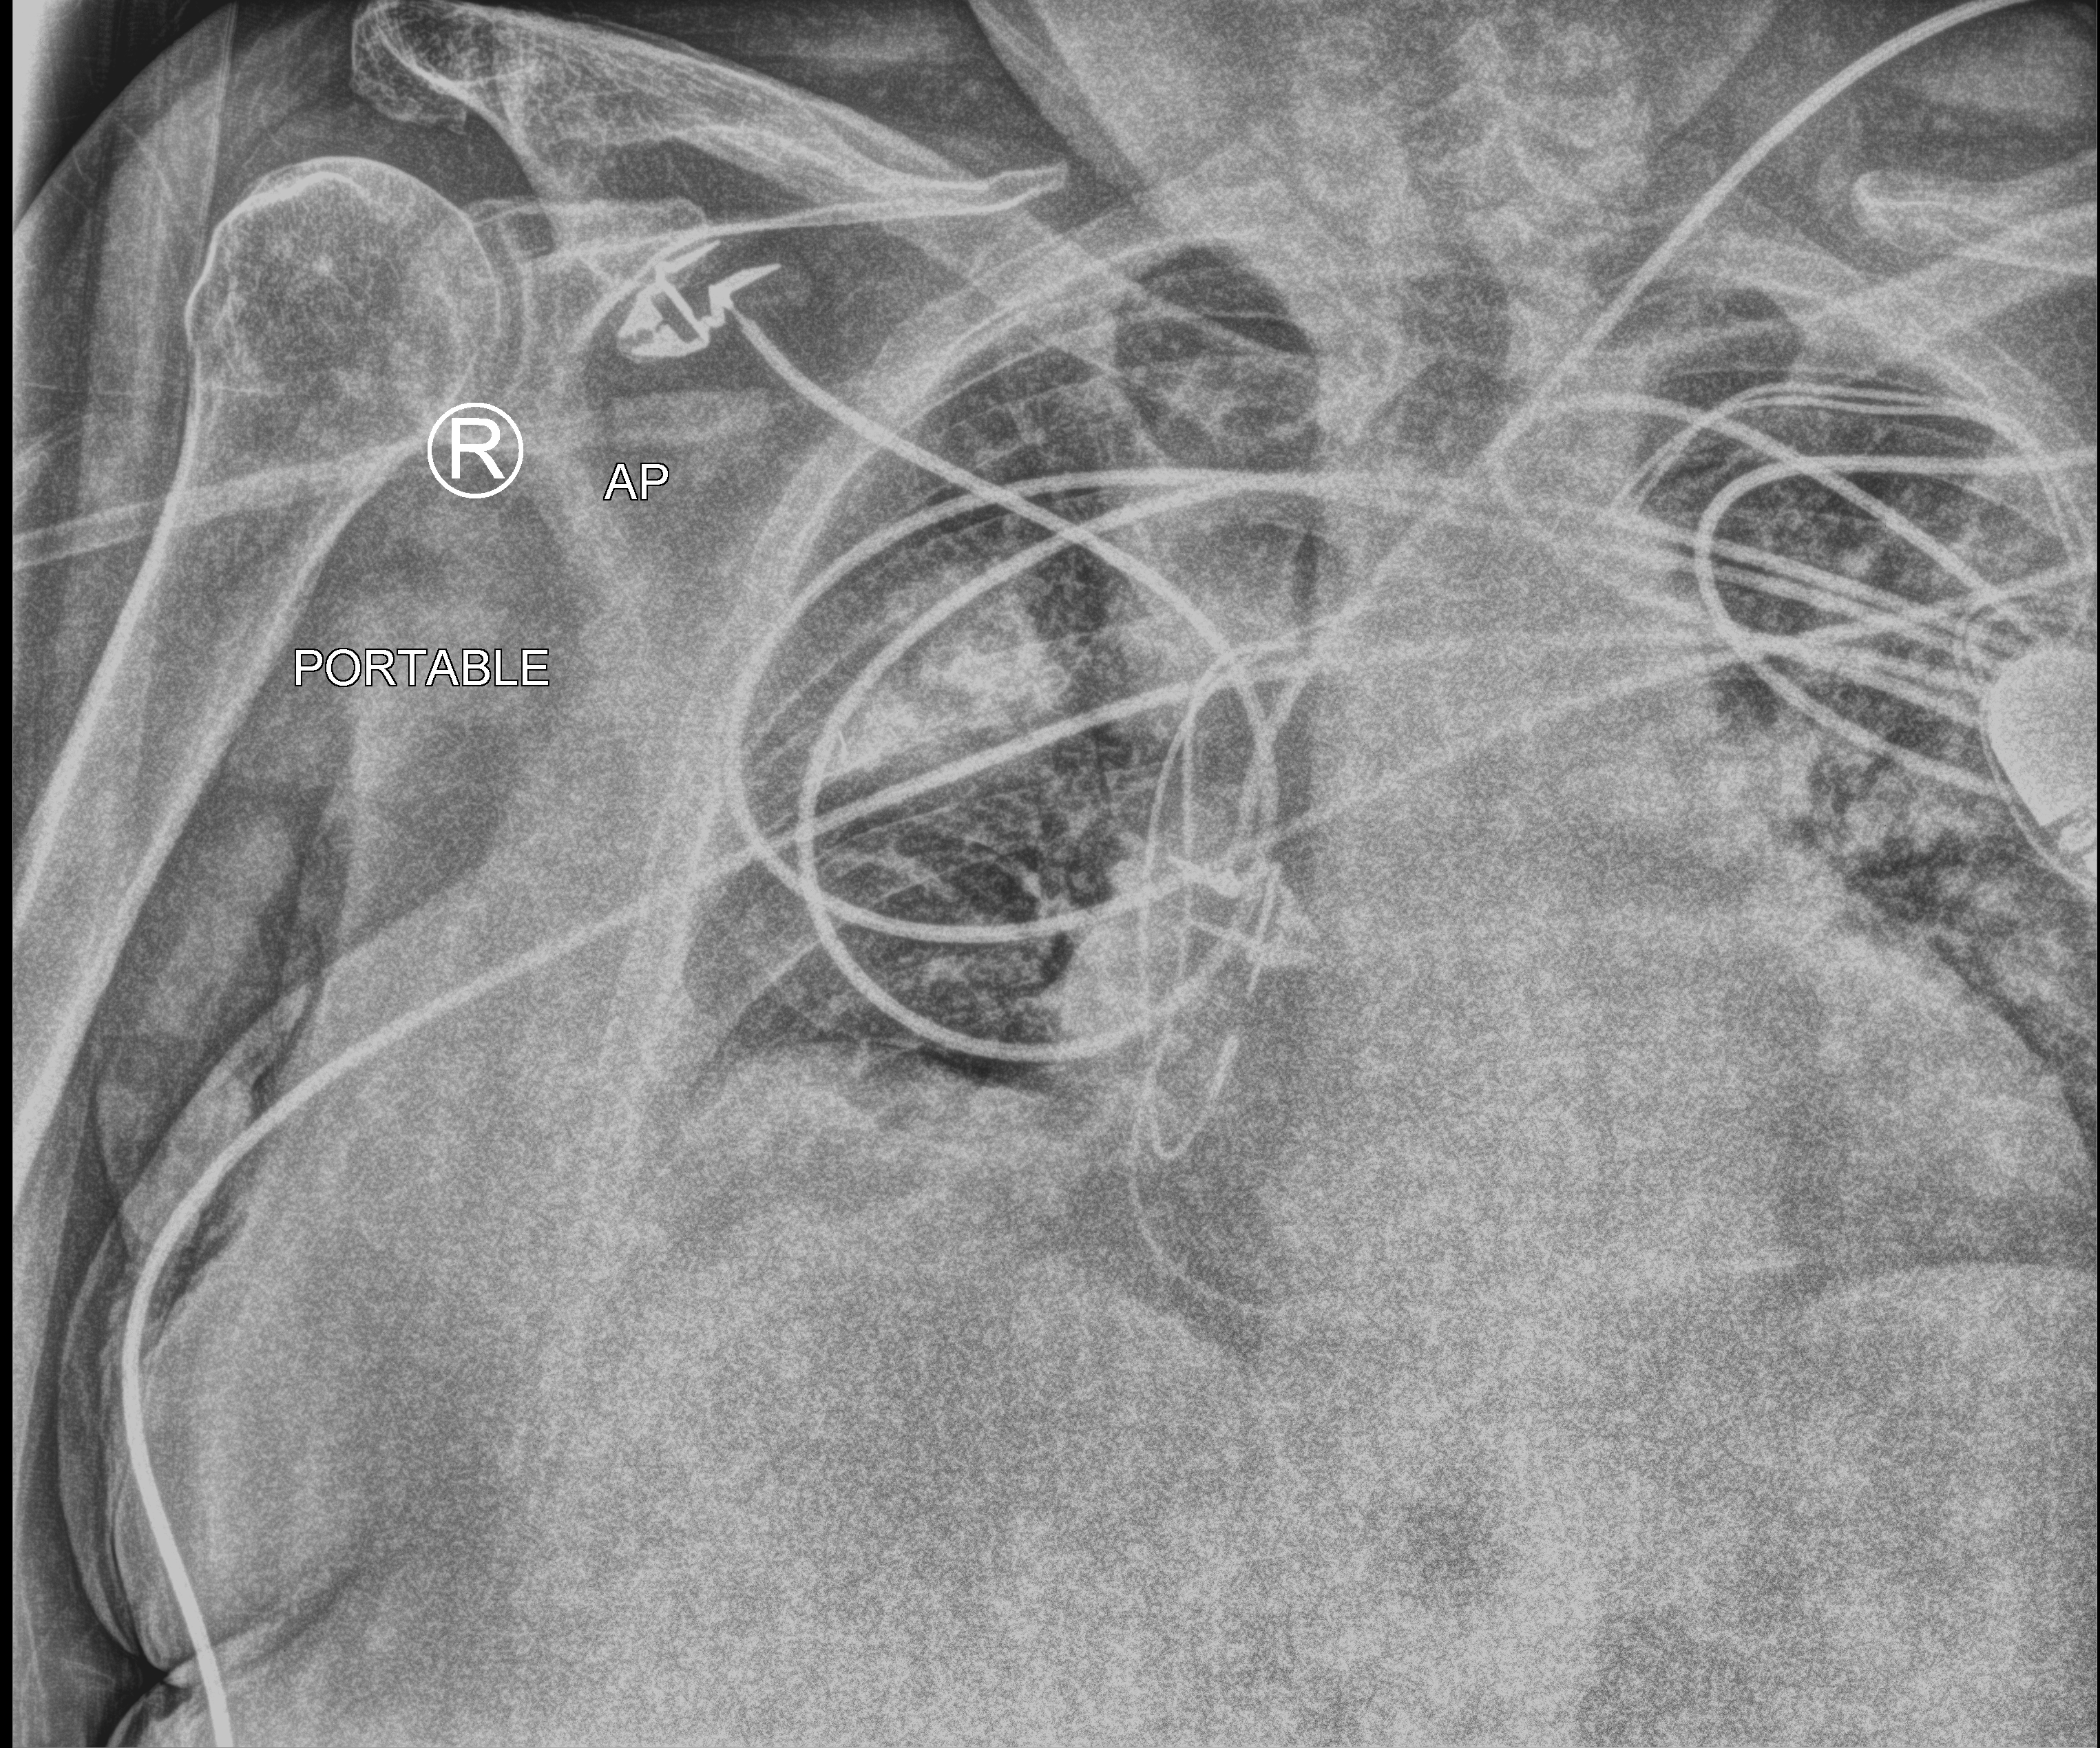
Bedside chest radiograph (computed radiography). Male patient hospitalised with COVID-19, age 75–90 years.
Admission-level facts for this patient (not findings on this image; timing relative to this image not recorded):
- length of hospital stay: 15 days
- chronic kidney disease (admission record): no
- admitted to intensive care during this hospital stay: no